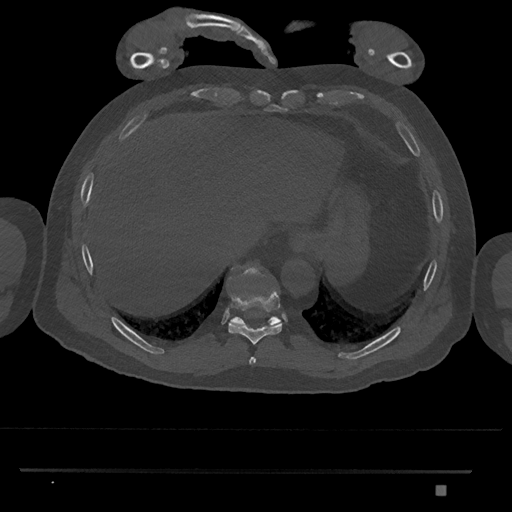
CT including the spine, one axial slice; position 1041 of 1134 along the scan axis; bone window (W 1800 / L 400 HU); 512 × 512 image matrix, field of view 429 × 429 mm. Male patient, age 65 years. Case-level facts recorded for this patient, not image findings: primary cancer: prostate.
Outlined on this slice (semi-automatic segmentation, software-assisted and operator-edited):
- T10 vertebra: bounding box (x1, y1, x2, y2) in pixels: (228, 265, 282, 327)
- T8 vertebra: (249, 357, 256, 365)
- T9 vertebra: (228, 290, 282, 345)